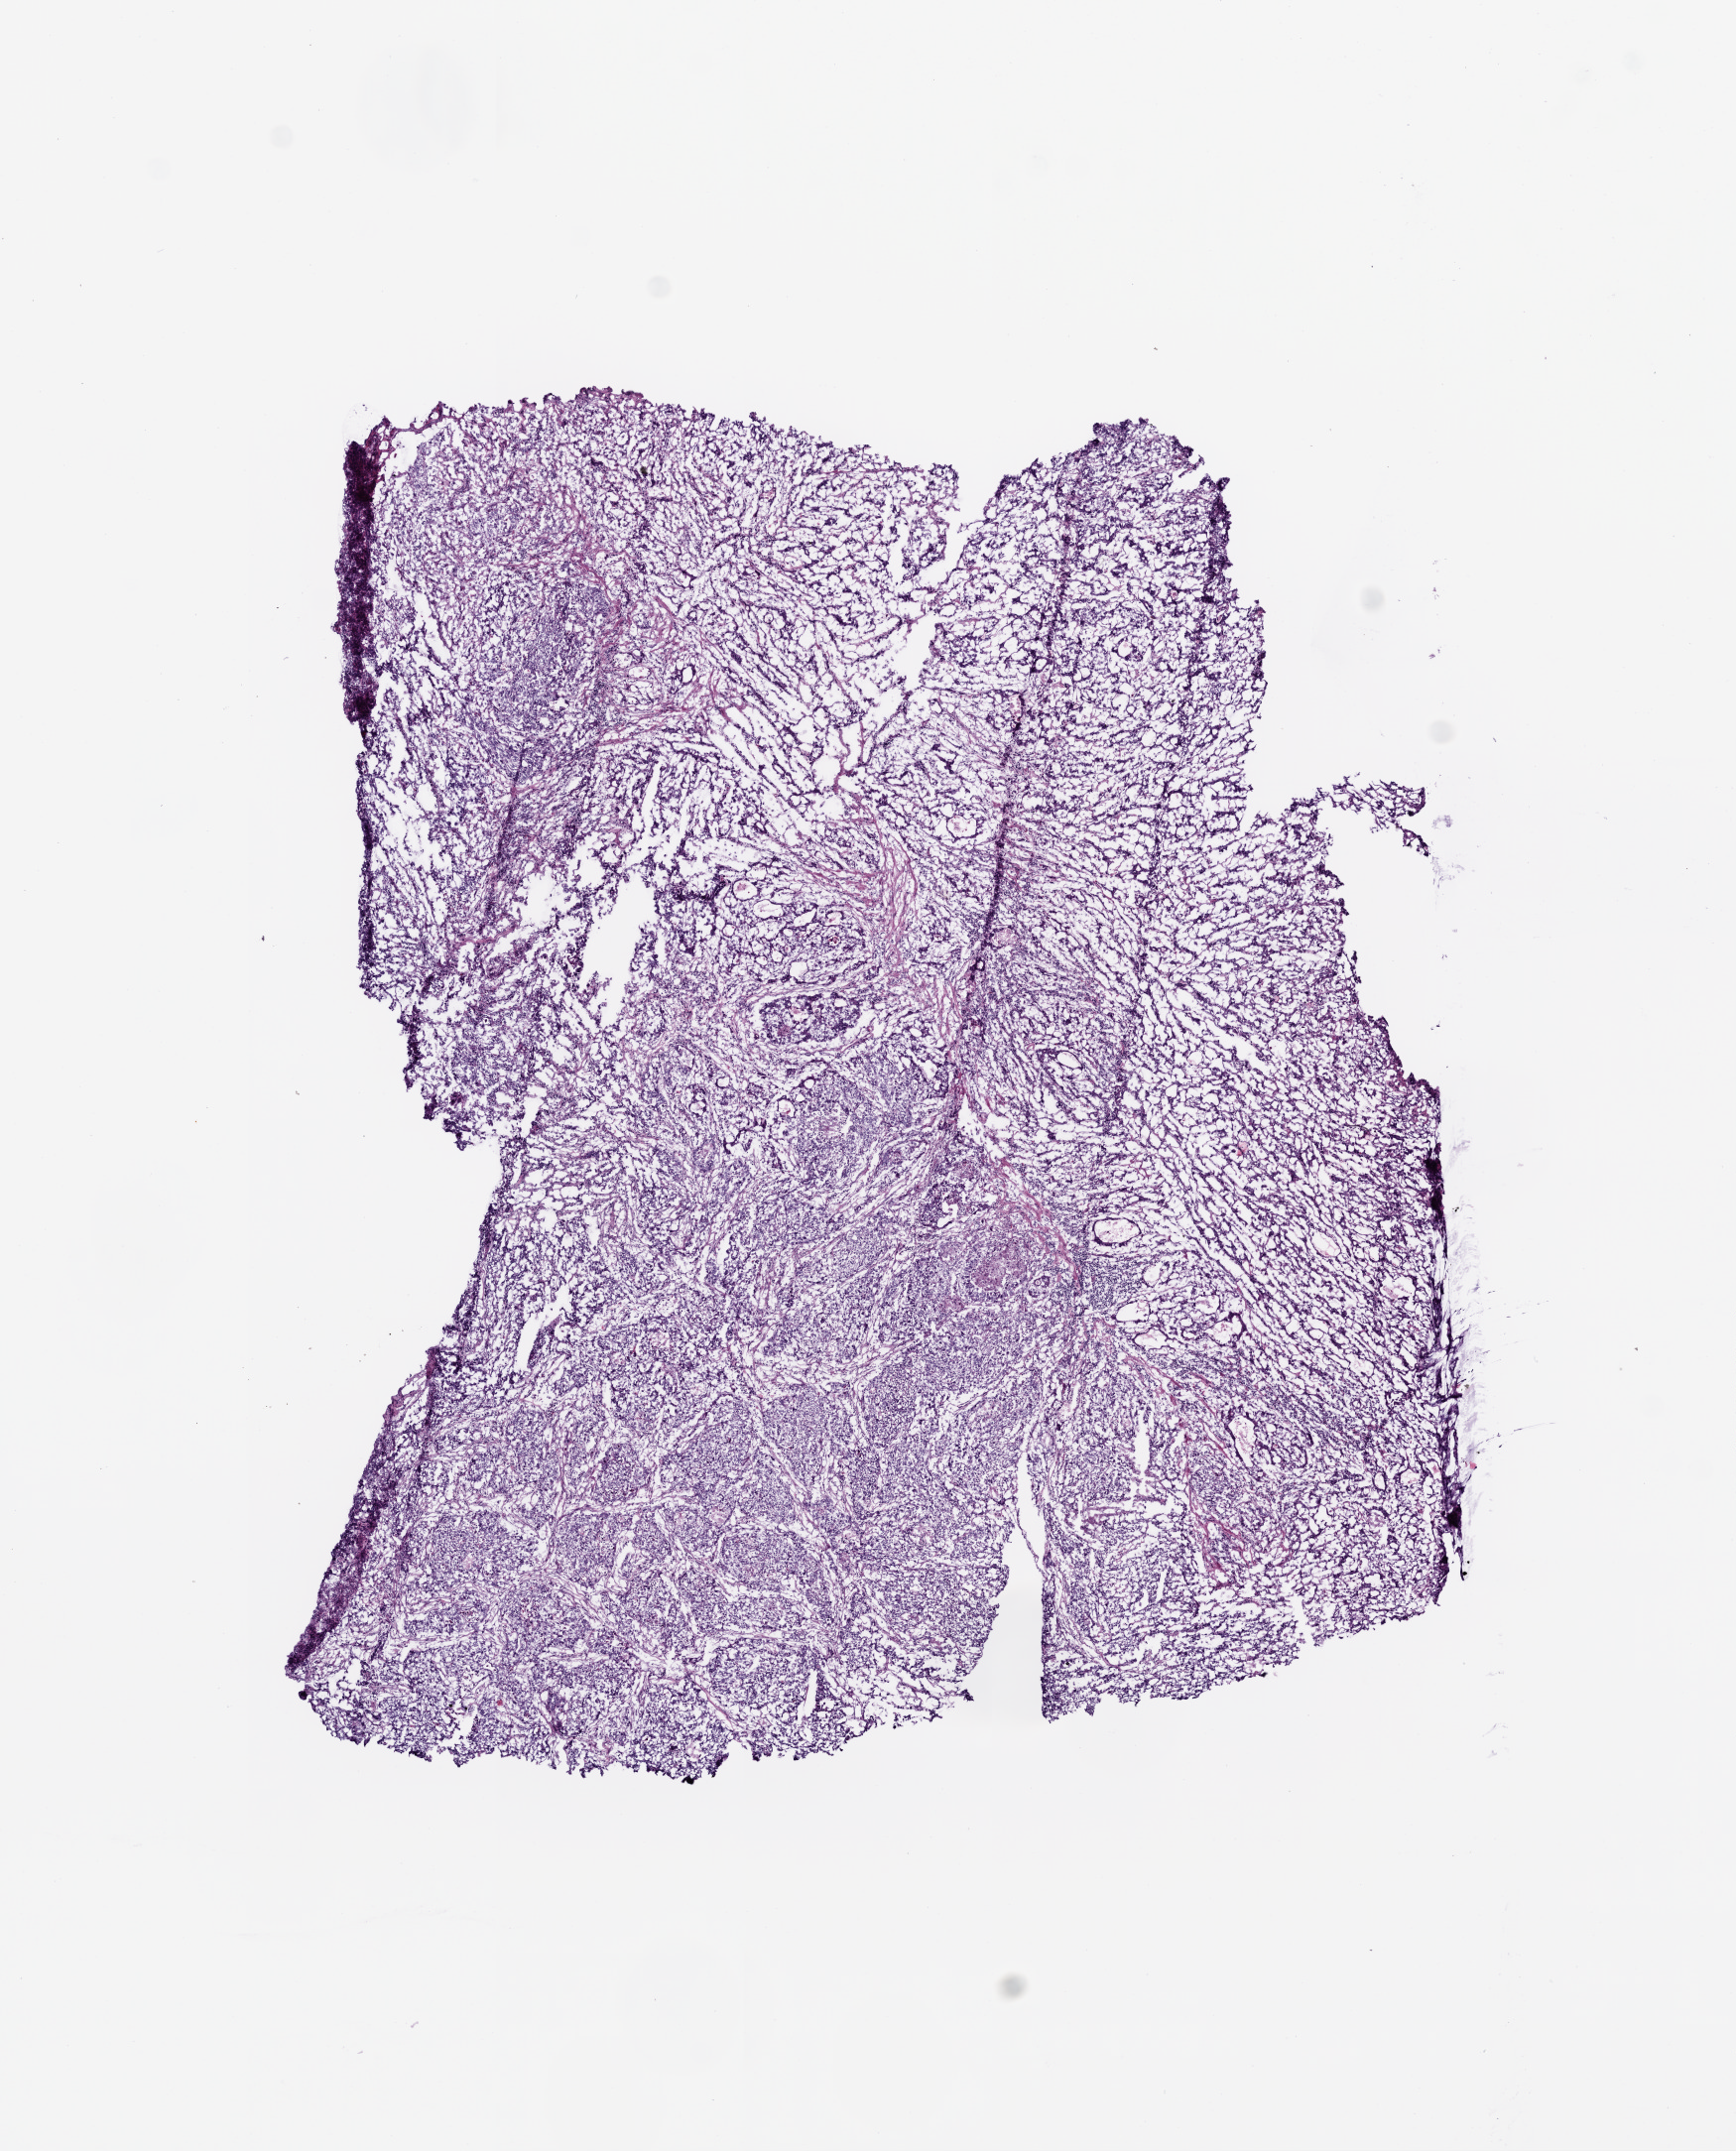
Digitized Hematoxylin and eosin (H&E) stained tissue section (whole slide), a low-resolution overview of the entire scanned area, about 7.0 x 8.7 mm. Frozen section from the top of the tissue portion. Stomach, primary tumour sample. Patient: male, age at initial diagnosis 79 years. Histologic grade: G2 (moderately differentiated). Pathologist review of this section (percent, as recorded): tumour cells 95%, tumour nuclei 74%, normal cells 0%, stromal cells 1%, necrosis 4%. Inflammatory infiltration, as recorded: lymphocyte infiltration 4%, neutrophil infiltration 3%.
Diagnosis: Adenocarcinoma, NOS (gastric antrum). TNM: T3 N2 M0. AJCC pathologic stage: IIIB (6th edition).